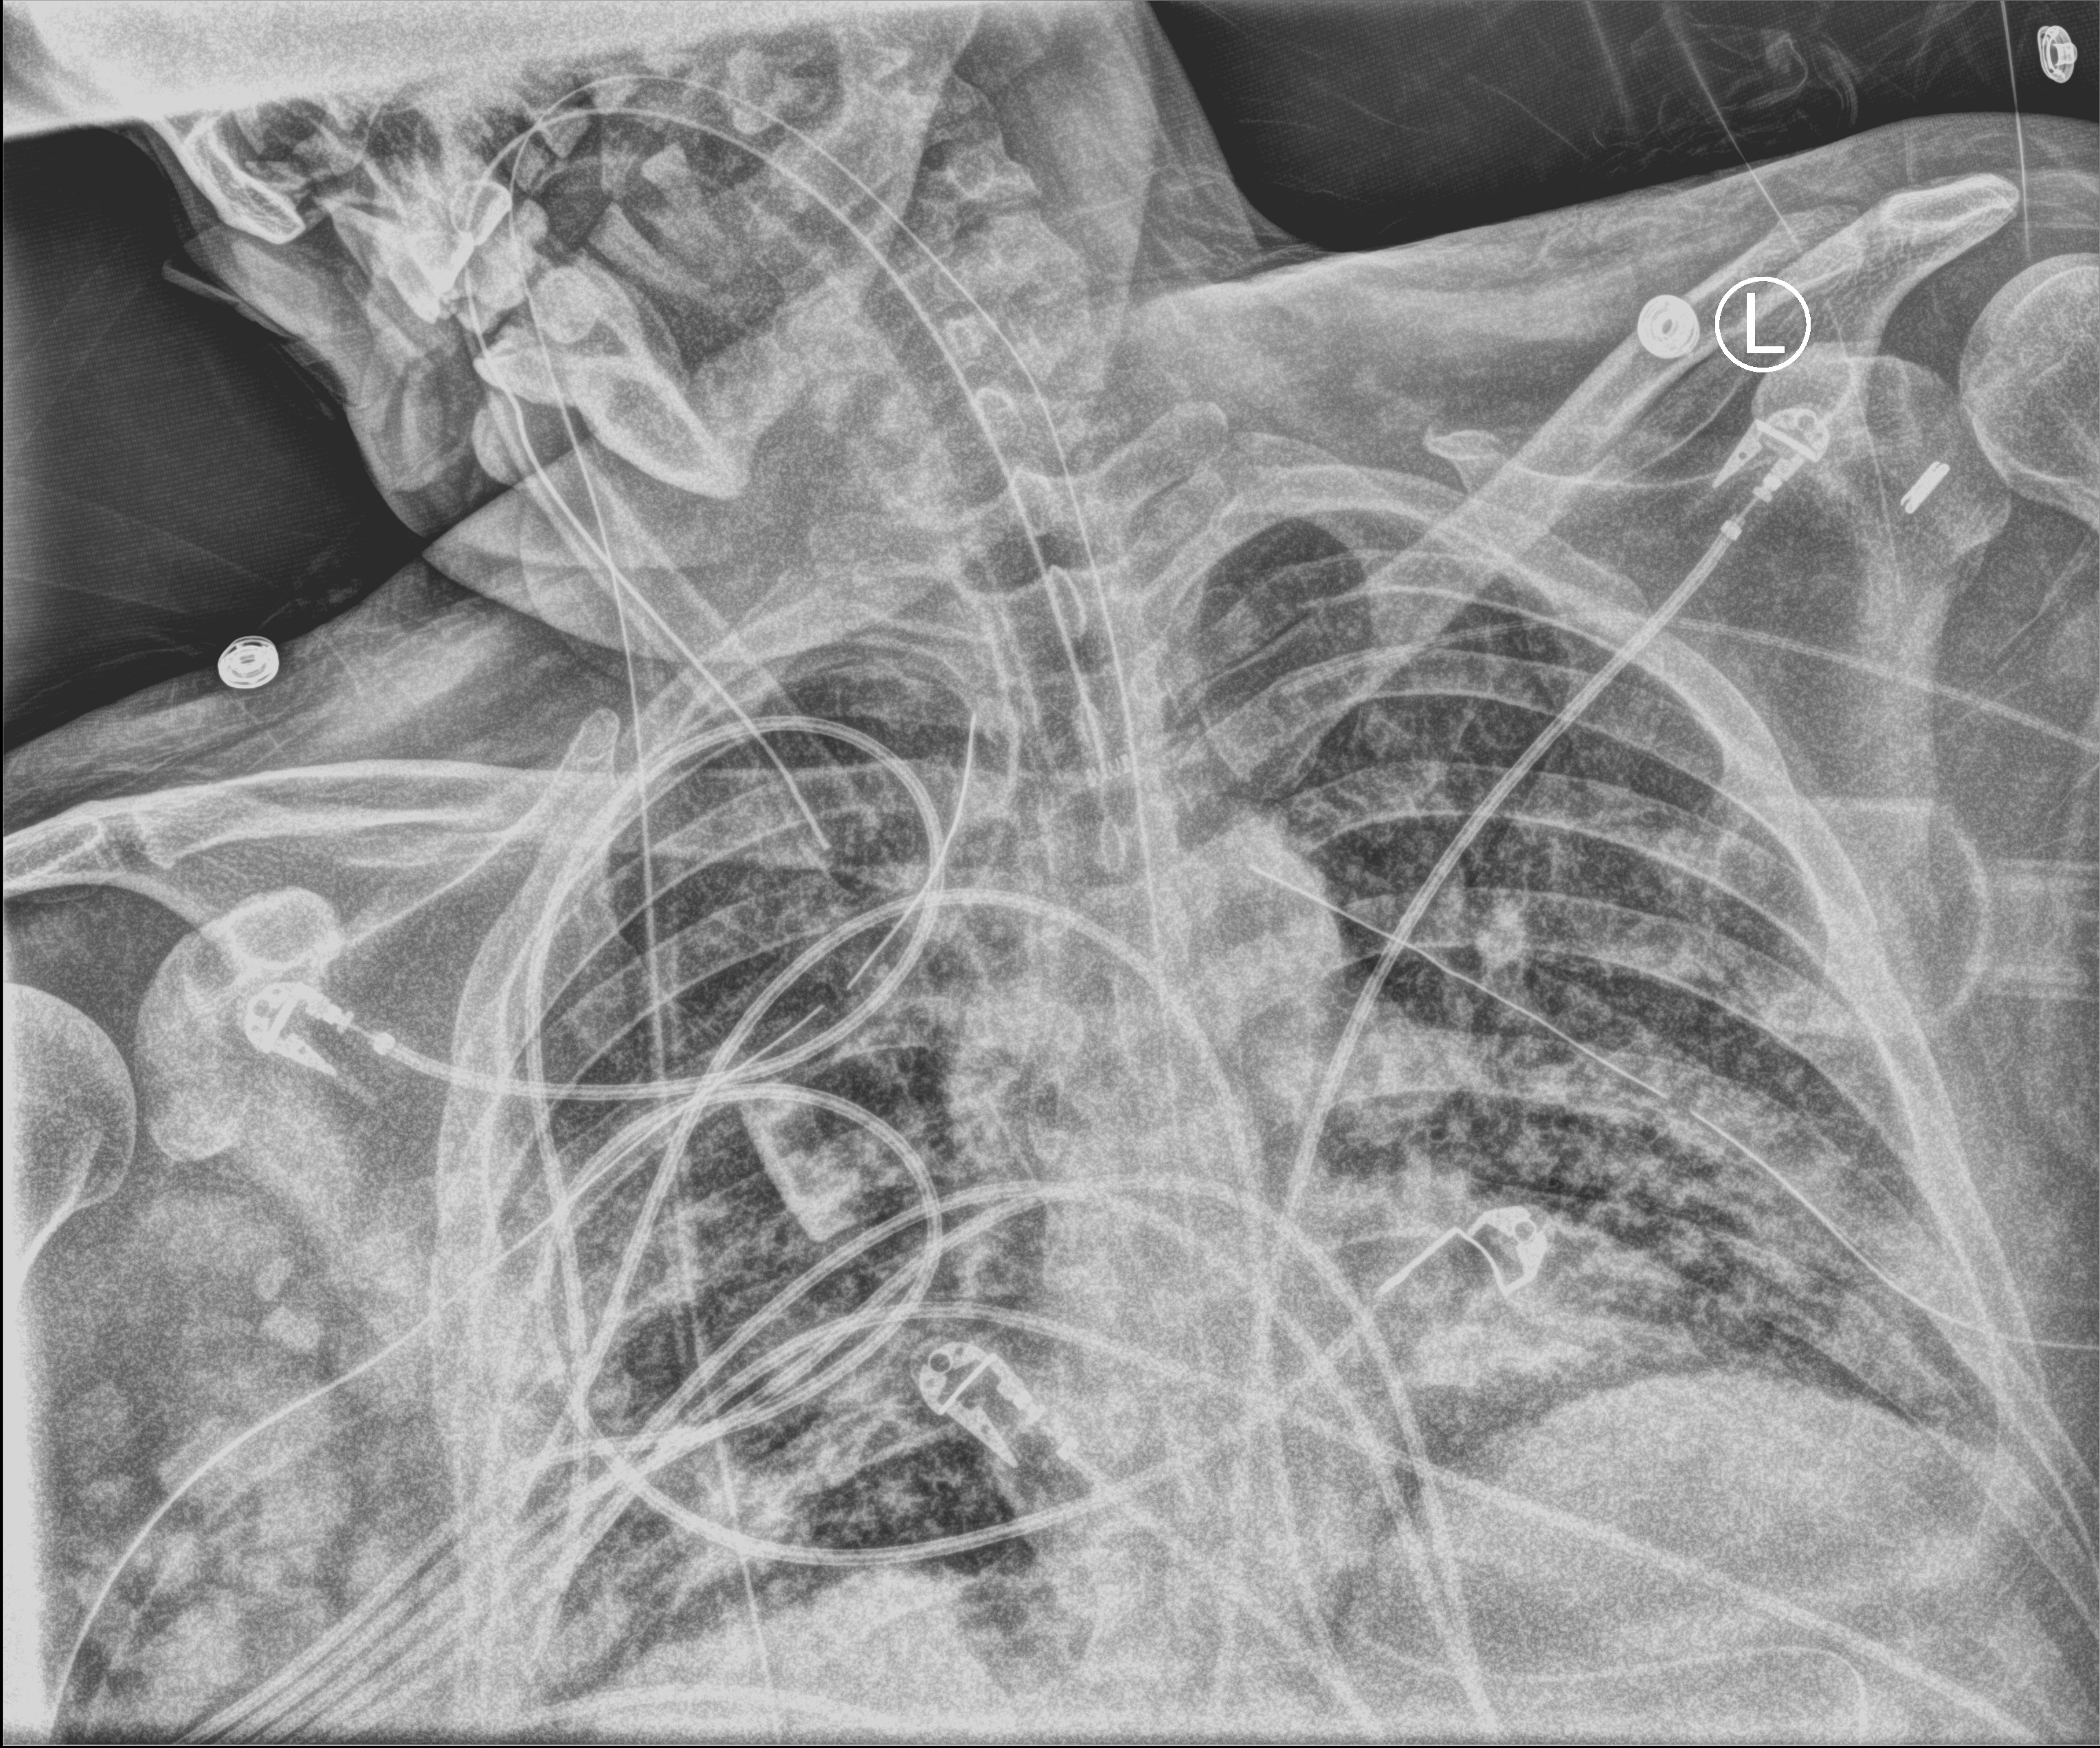
Bedside chest radiograph (computed radiography). Patient hospitalised with COVID-19; male, aged 18–59 years.
Hospital-stay facts (about this admission, not read from this image; timing relative to this image not recorded): mechanically ventilated during this hospital stay: yes; admitted to intensive care during this hospital stay: yes; chronic kidney disease (admission record): no.